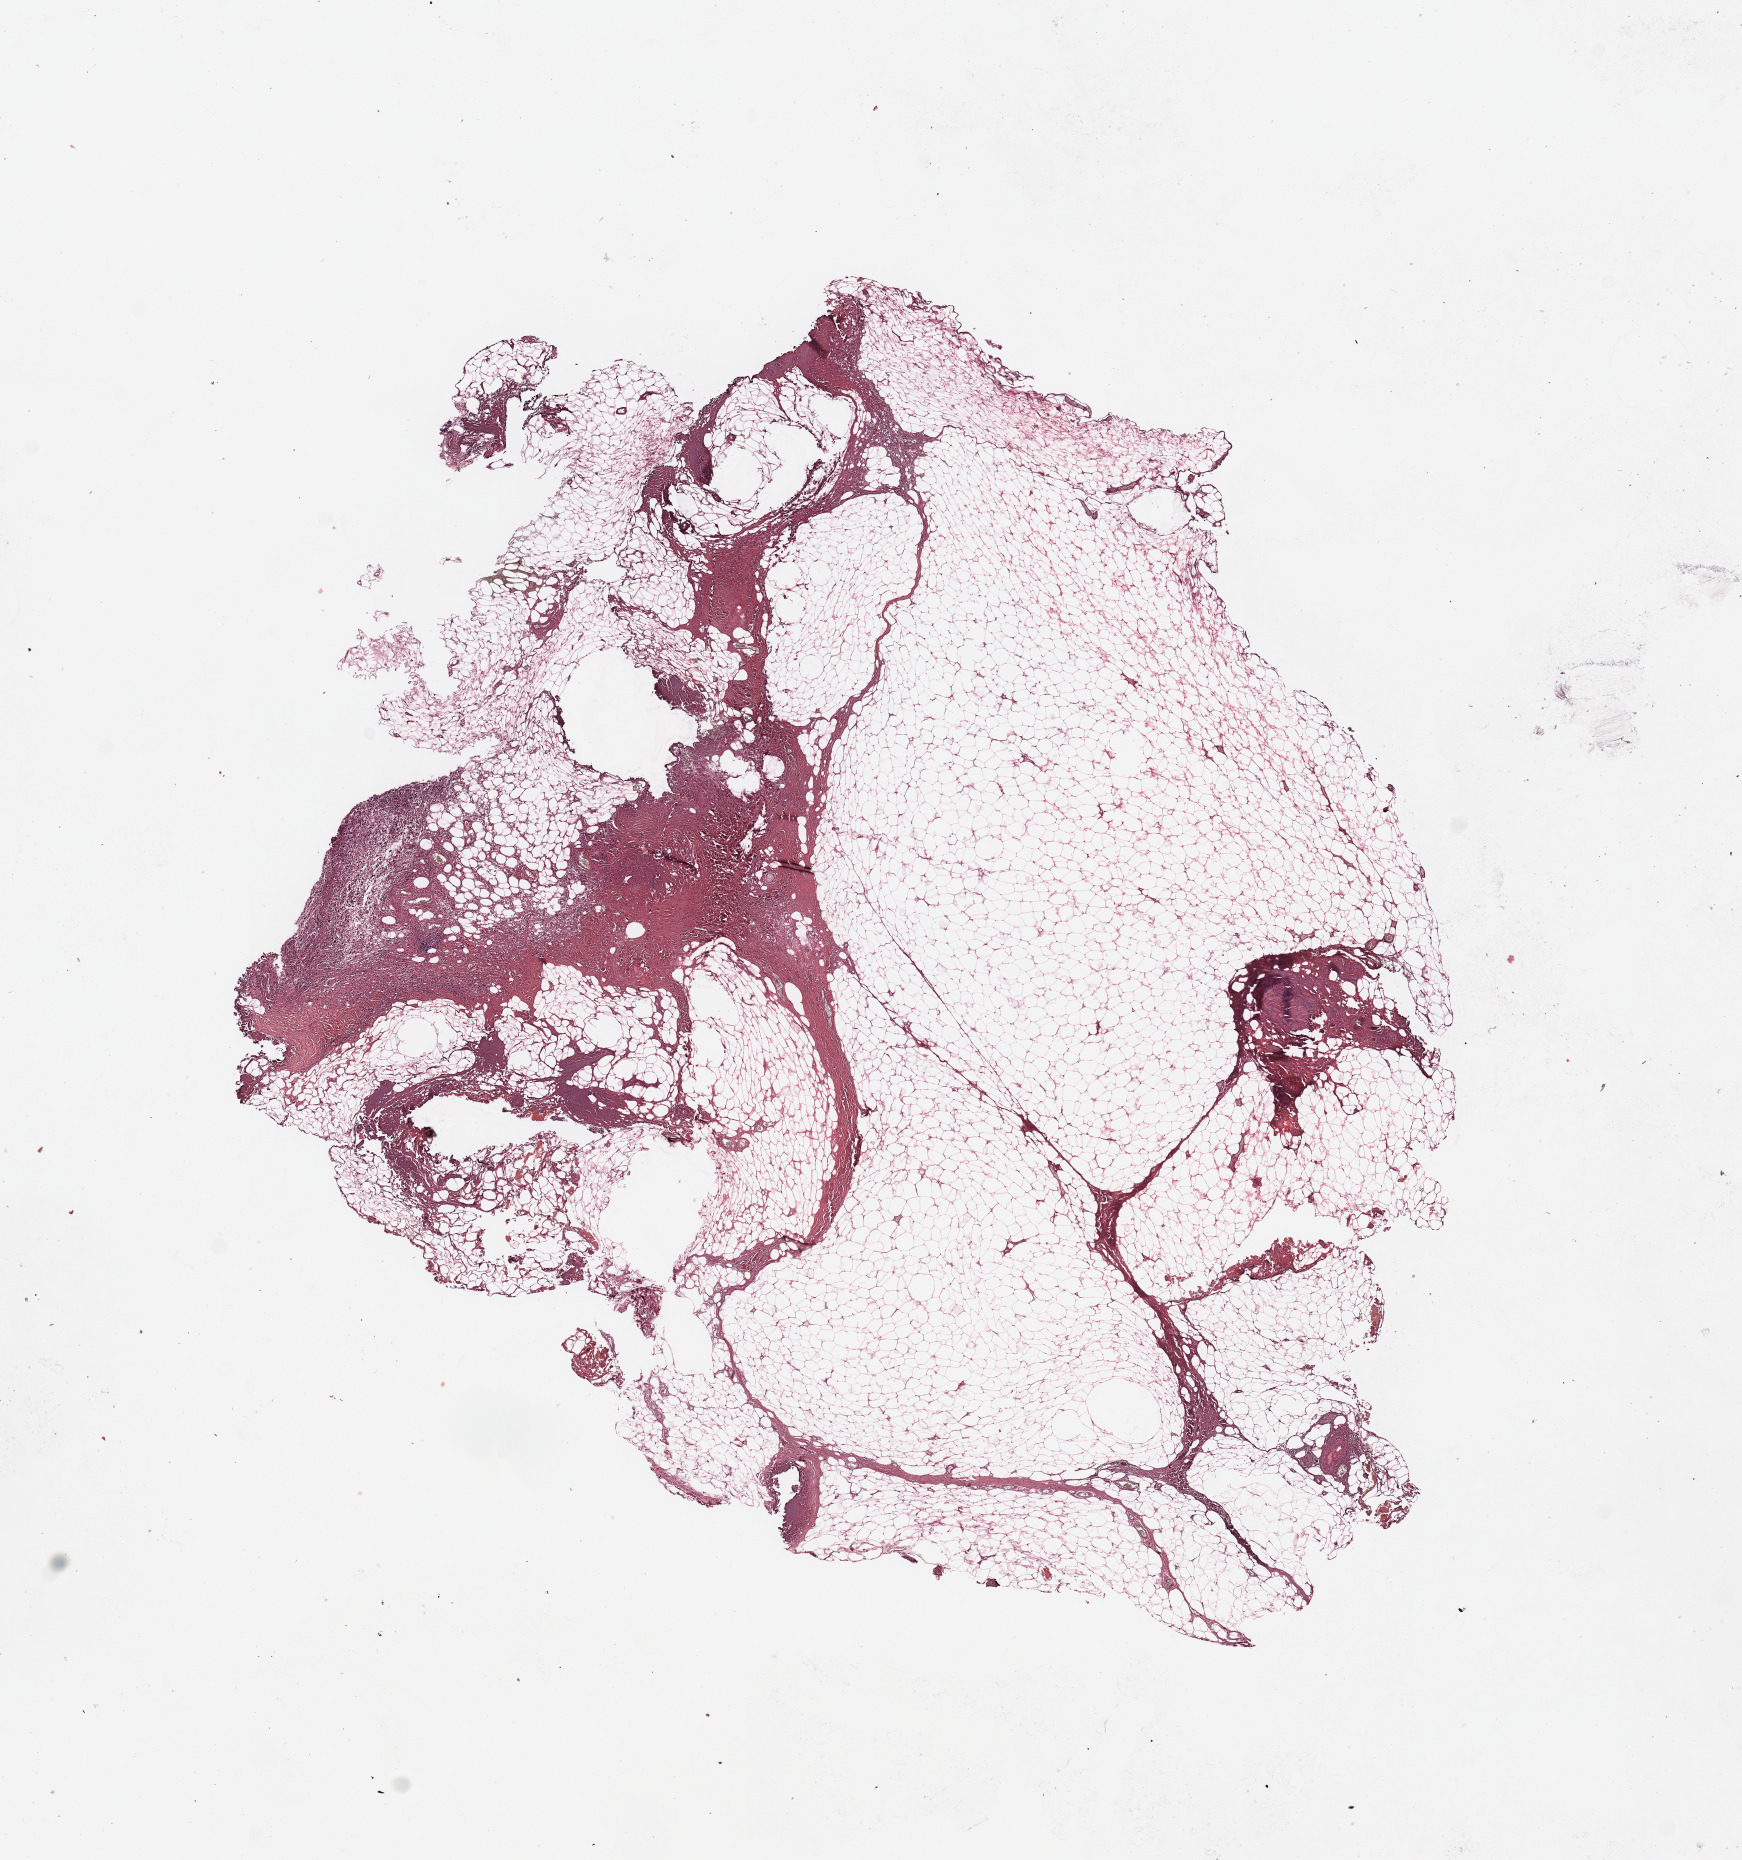
Whole-slide histology image, H&E-stained — low-resolution overview of the scanned area, about 13.8 x 14.7 mm. Normal (non-tumour) tissue sample. 58-year-old female patient.
This section: normal (non-tumour) tissue from the same patient. Patient diagnosis (cohort enrolment): sarcoma (site not recorded at cohort level).